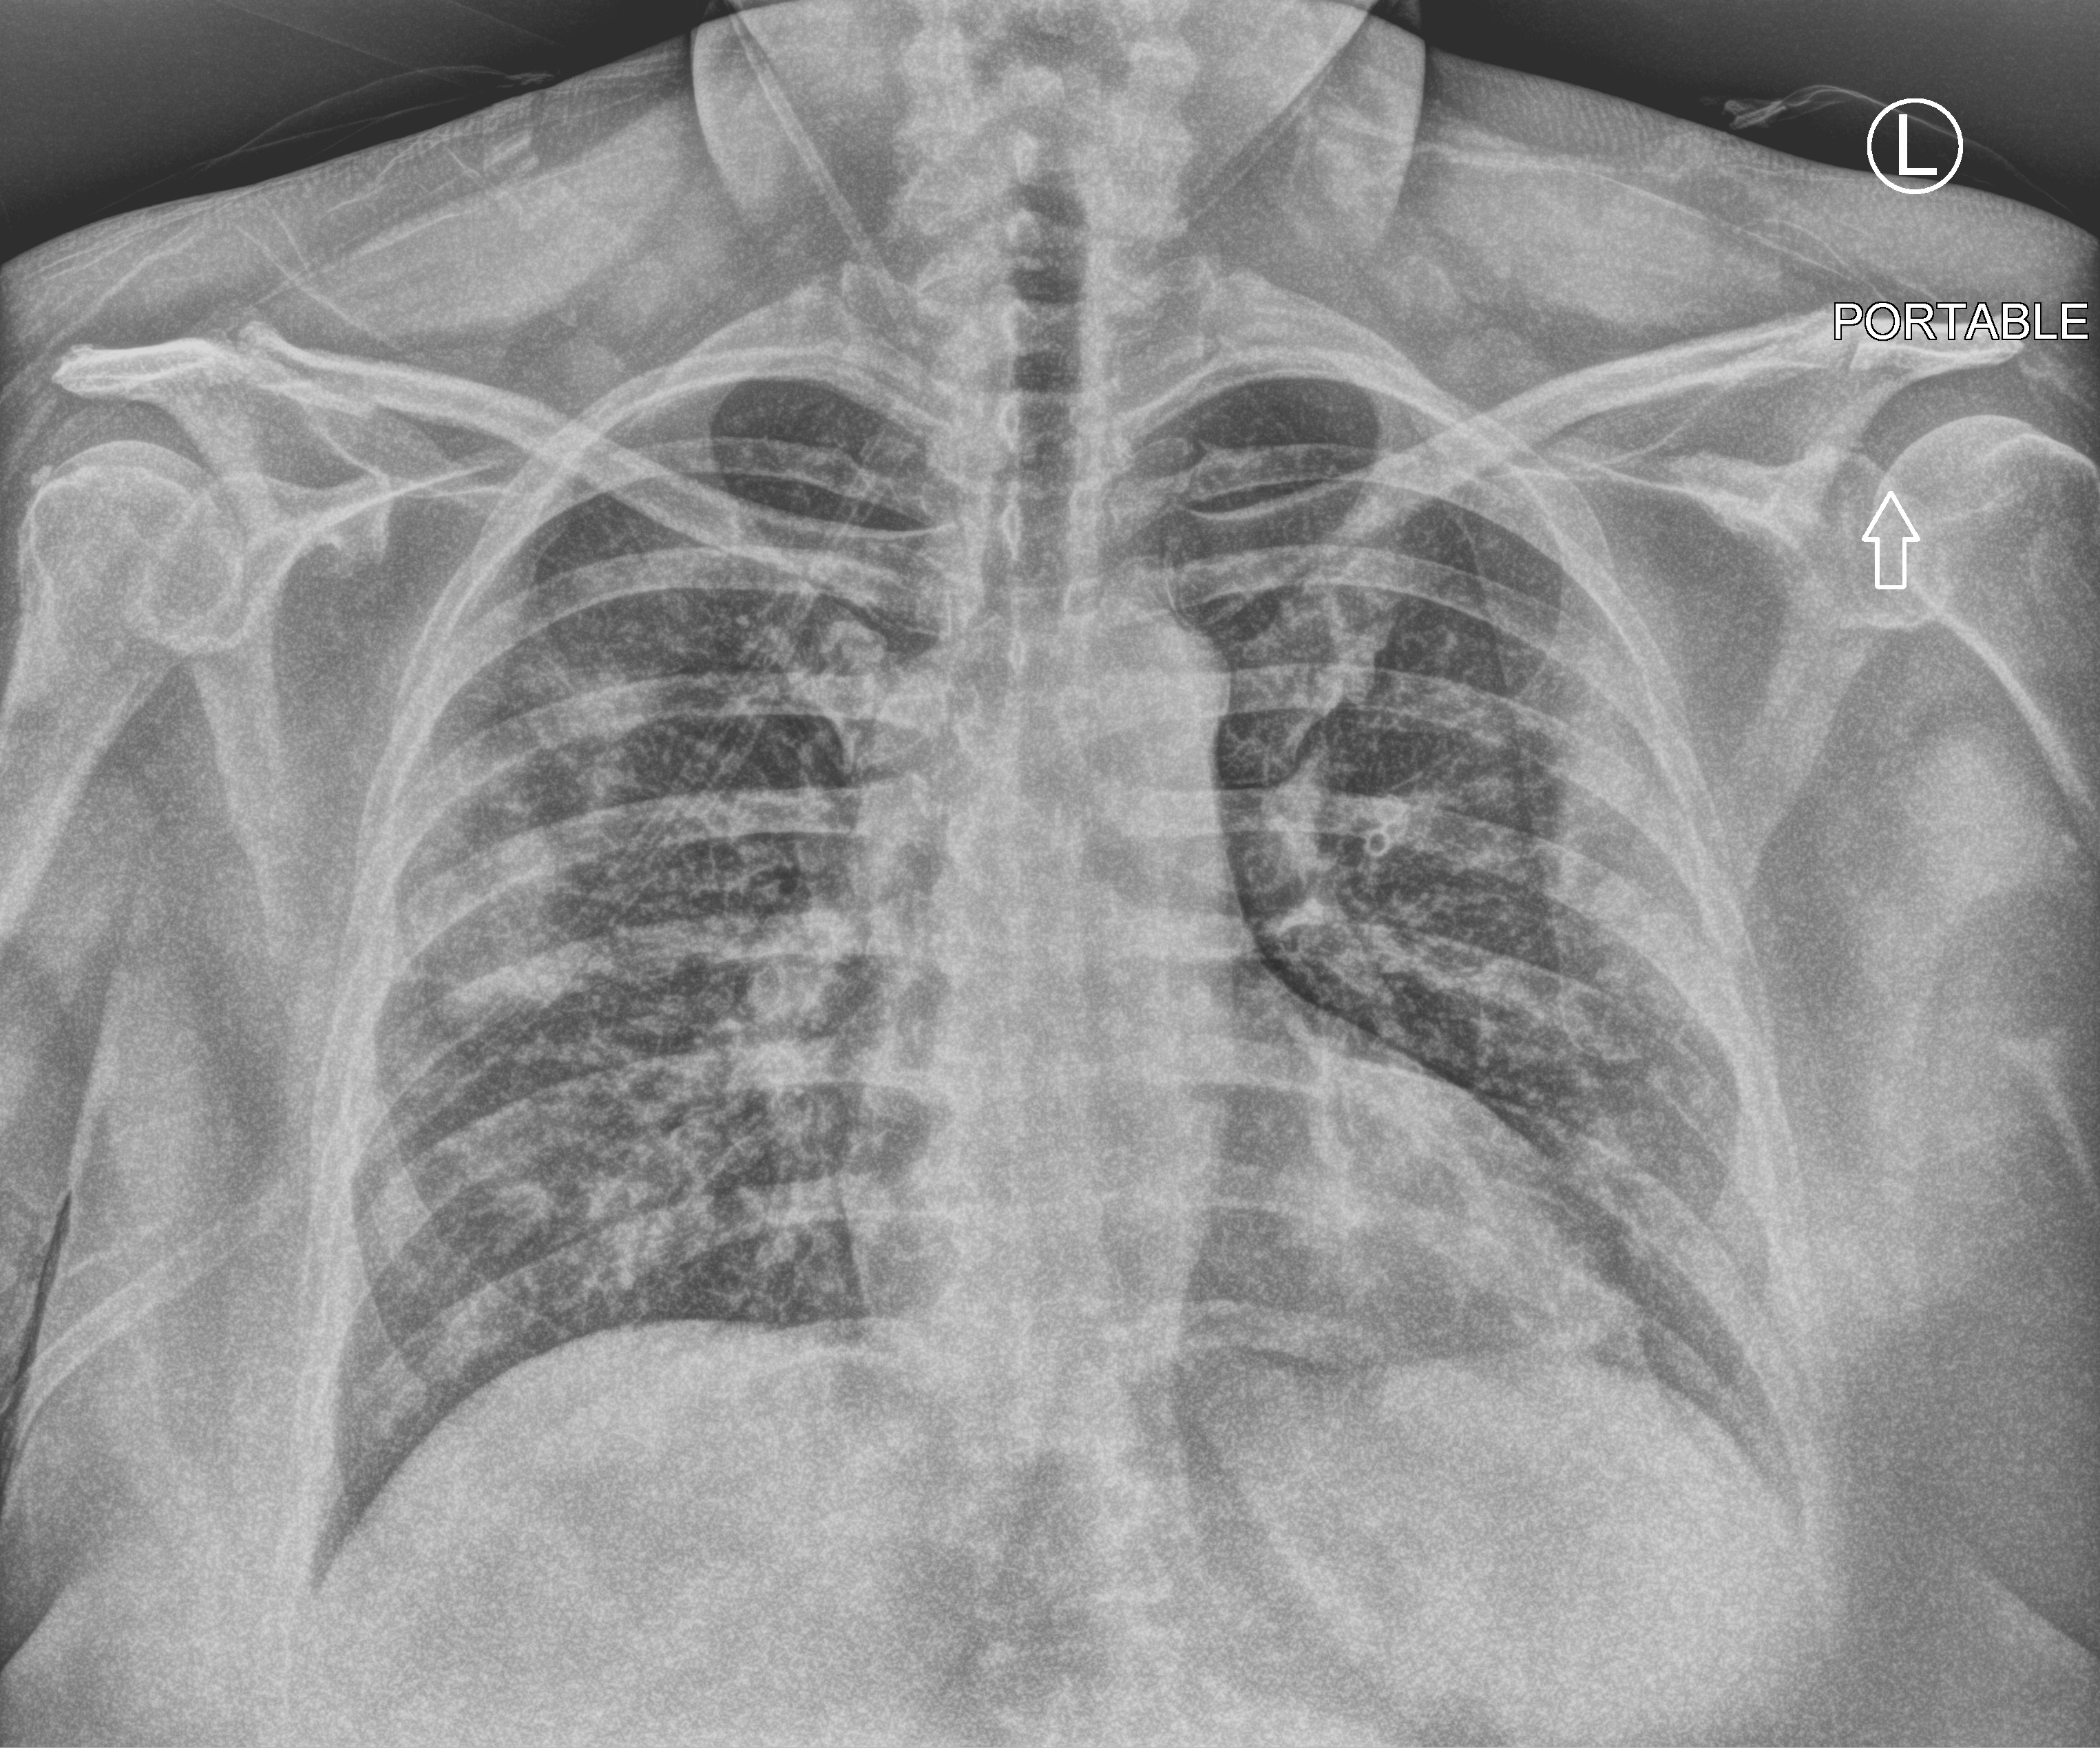
Bedside chest radiograph (computed radiography), anteroposterior (AP) projection. Patient hospitalised with COVID-19; female, aged 18–59 years.
Hospital-stay facts (about this admission, not read from this image; timing relative to this image not recorded): chronic kidney disease (admission record): no; smoking status (admission record): current.